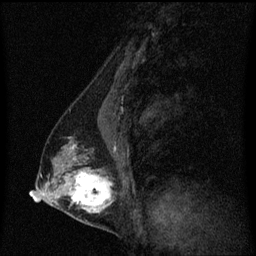
Breast MRI (dynamic contrast-enhanced), one sagittal slice. Position 29 of 60 along the scan axis. Dynamic contrast-enhanced series, image 2 of 3 at this slice position (ordered by acquisition). 1.5 T. TE 4.2 ms, TR 8.4 ms. 256 × 256 image matrix. Patient: female, 40 years. From the clinical record (not read from this slice): setting: breast cancer imaged before/during neoadjuvant chemotherapy; receptor status: triple-negative.
Structures marked on this image (semi-automatically segmented with operator editing):
- analysis volume of interest (the breast-tissue region the enhancement analysis was run in; not a lesion): bounding box (x1, y1, x2, y2) in pixels: (44, 128, 119, 221)
- tumour enhancement mask (voxels above the 70 % enhancement threshold inside the analysis volume of interest): (69, 170, 112, 213)